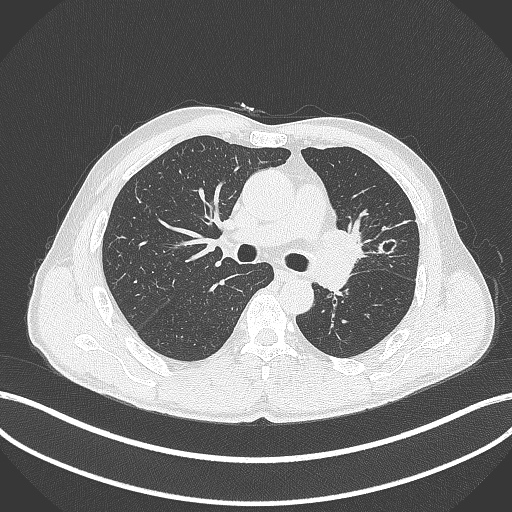
Chest CT, one axial slice; position 257 of 429 along the scan axis; lung window (W 1500 / L -600 HU); 1 mm slice thickness; 512 × 512 image matrix. Male patient, age 57 years. From the clinical record (not read from this slice): clinical TNM (as recorded): T2b N0 M0.
Structures marked on this image (rectangle marked by the reading radiologist):
- lung tumour (recorded histology: squamous cell carcinoma): box from (x=316, y=220) to (x=368, y=268) px